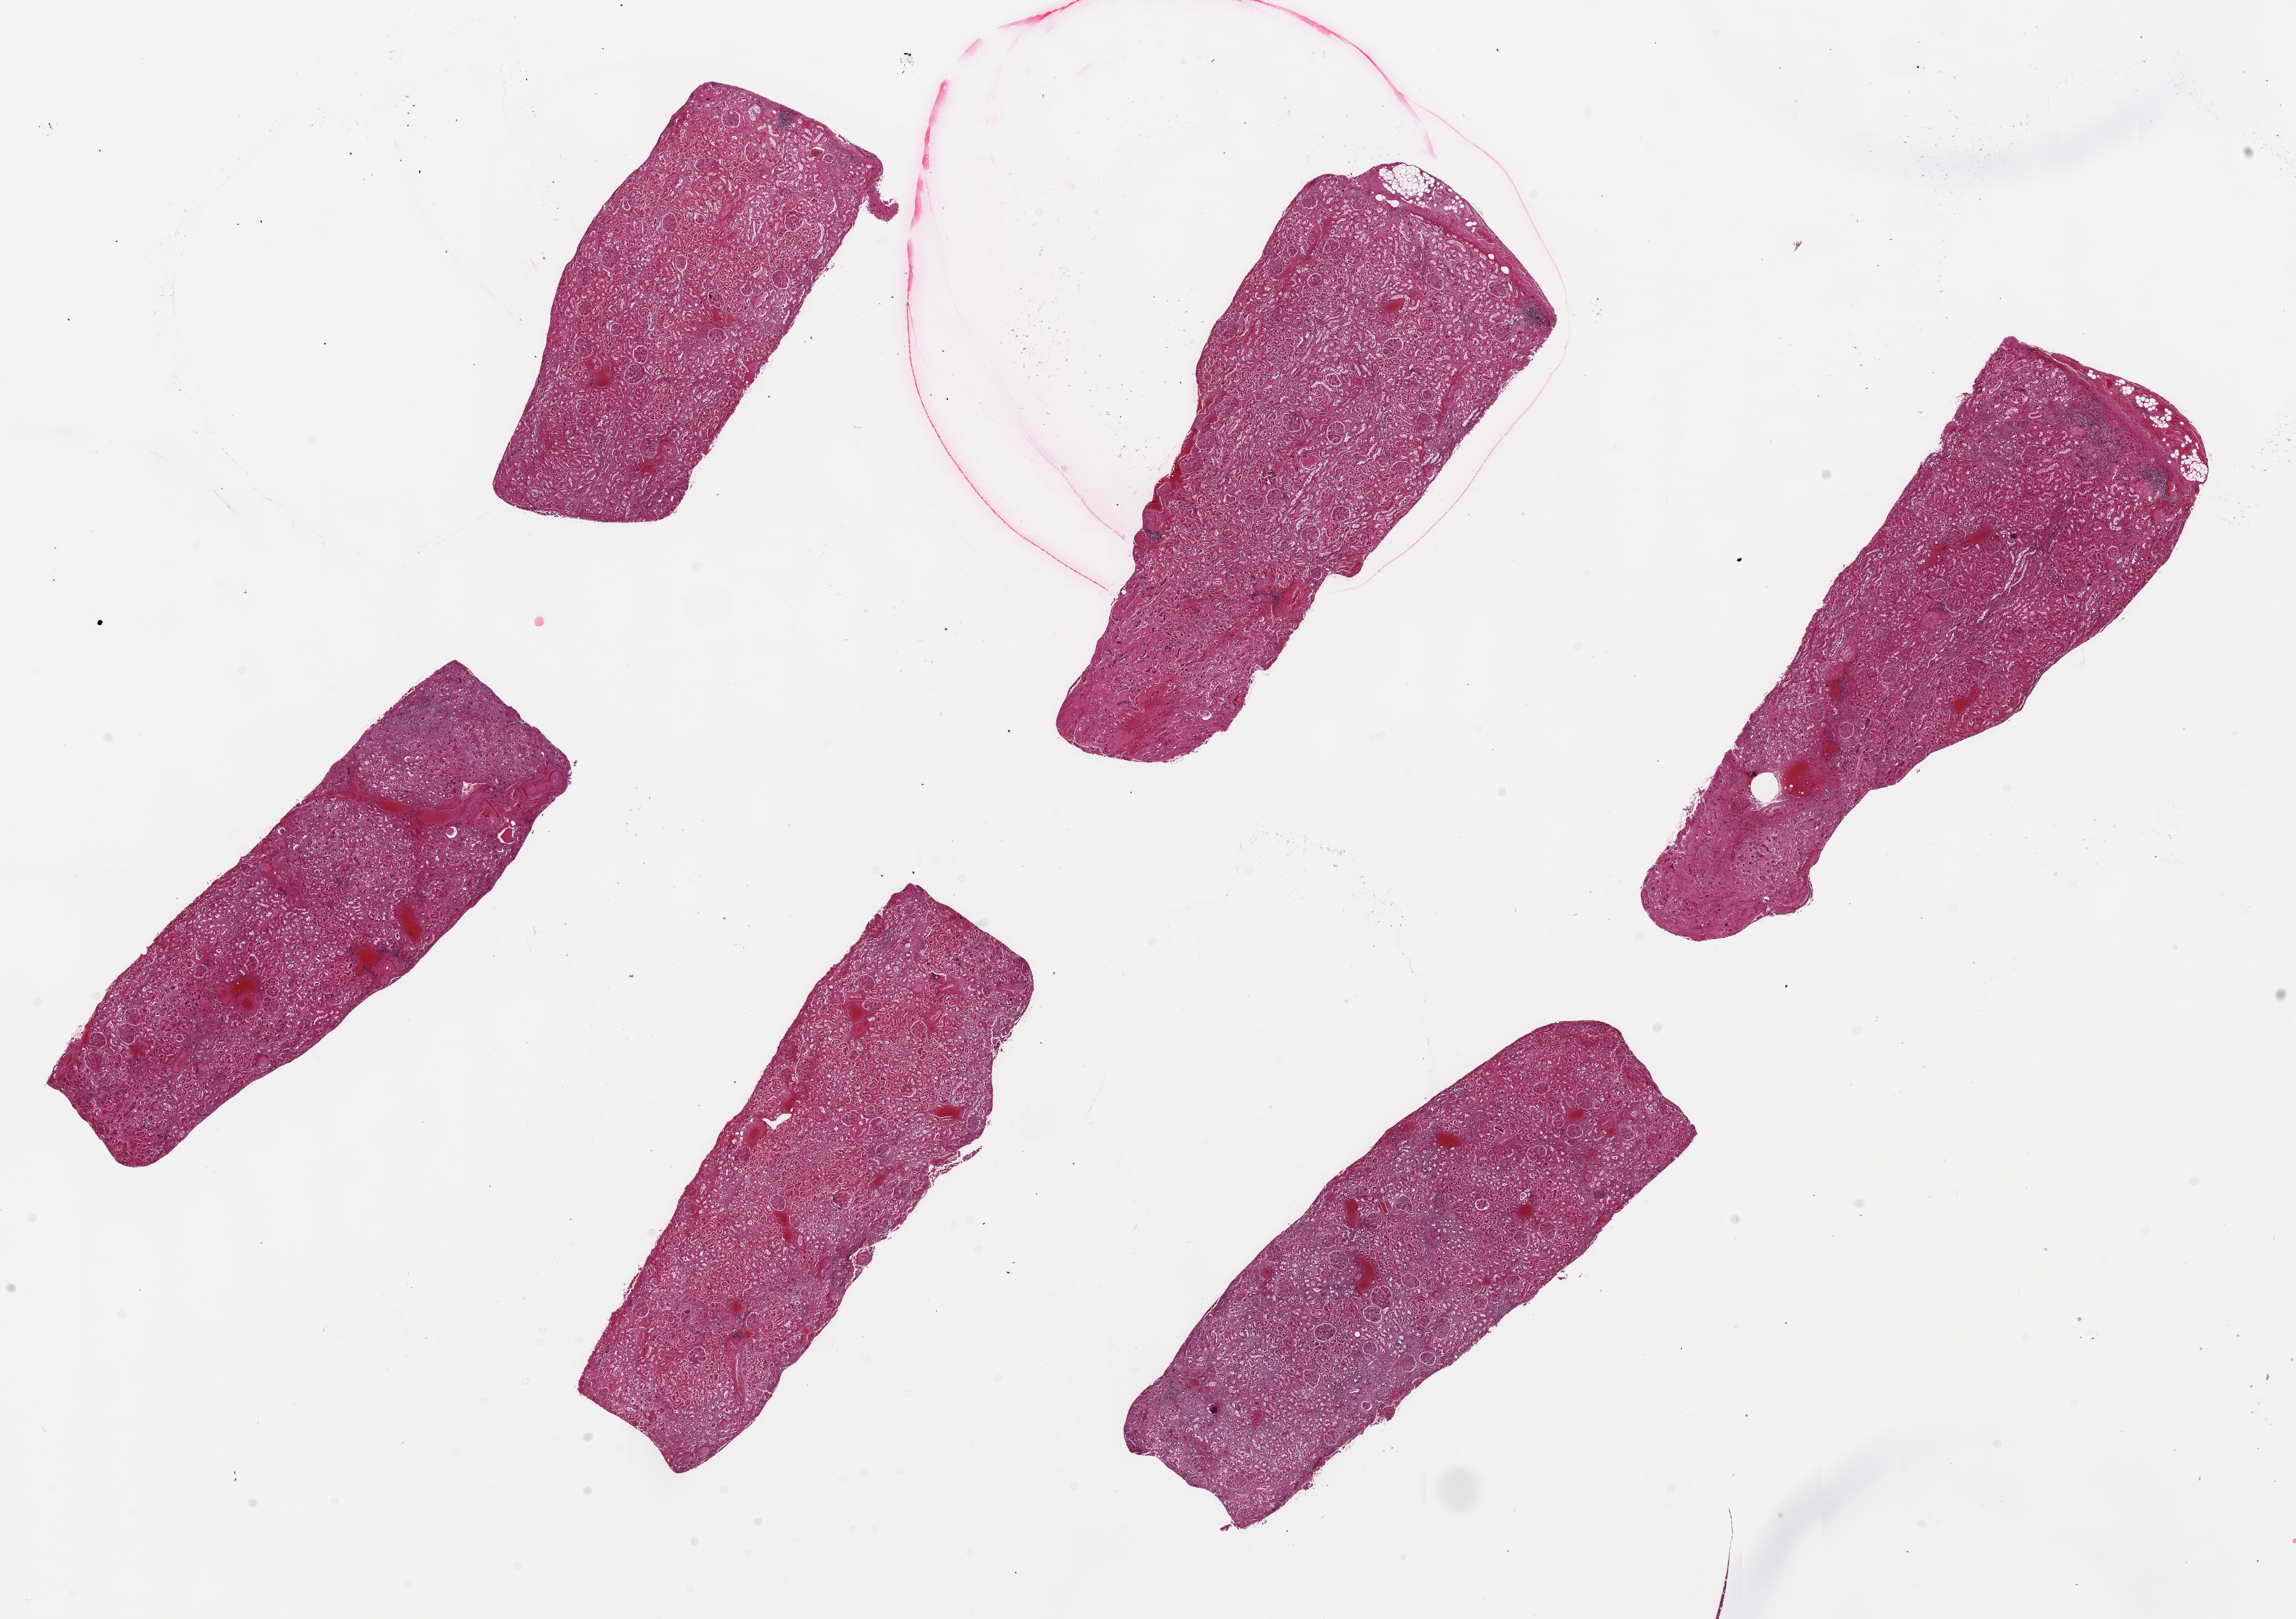
H&E whole-slide image — shown as a low-resolution overview of the whole scanned area (about 28.5 x 20.1 mm); PAXgene-fixed, paraffin-embedded tissue; section of renal cortex (target tissue); donor tissue sample. Donor: male.
• pathologist's review note for this sample: 6 pieces, up to 8x3mm; Patchy vascular and glomerular sclerosis